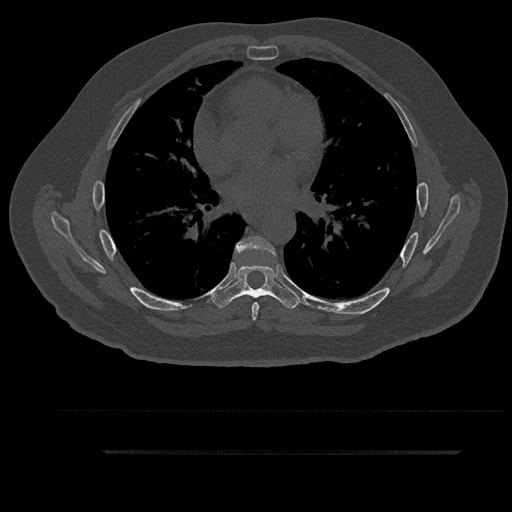
CT including the spine, one axial slice; slice 547 of 797 in the series (ordered by position); reconstruction kernel Br40s/3; bone window (W 1800 / L 400 HU); 512 × 512 image matrix, field of view 432 × 432 mm. Male patient, age 63 years. From the clinical record (not read from this slice): primary cancer: renal; vertebrae with lytic lesions (as recorded): T8.
Structures marked on this image (semi-automatic segmentation, software-assisted and operator-edited):
- T6 vertebra: bounding box <236,236,275,321> (left, top, right, bottom; pixels)
- T7 vertebra: <212,265,299,309>